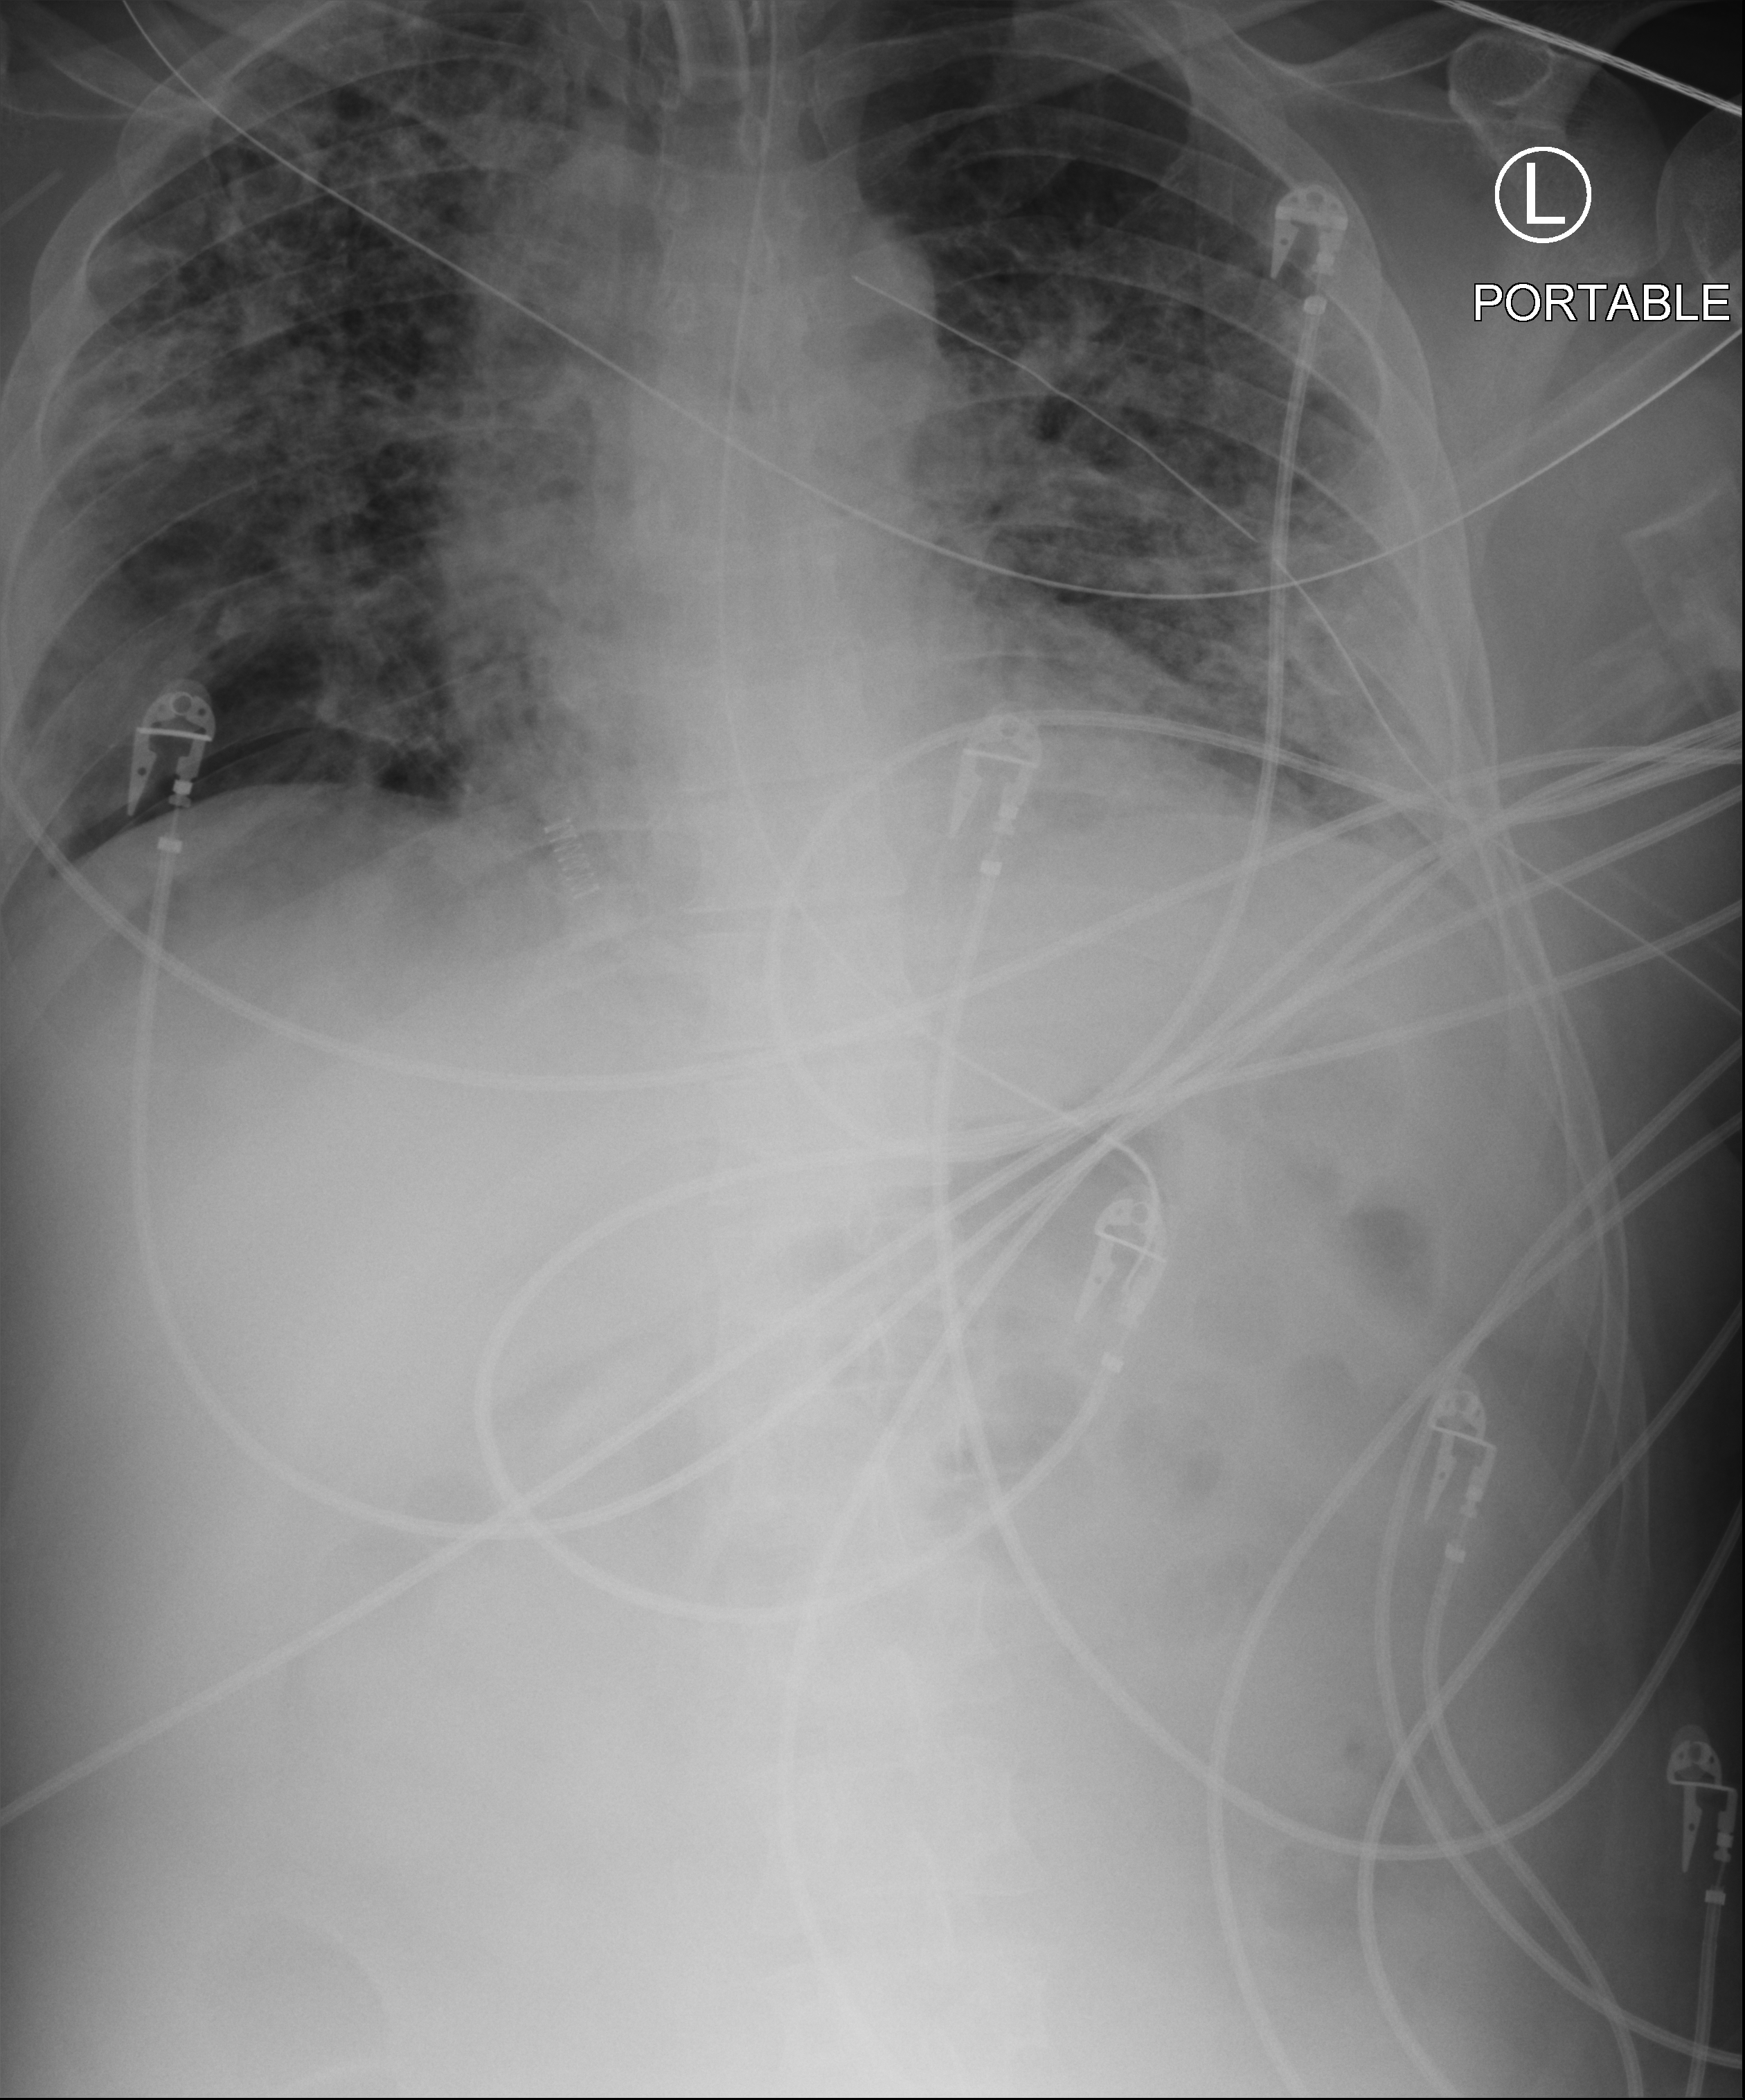
Bedside chest radiograph (computed radiography), anteroposterior (AP) projection. Patient hospitalised with COVID-19; male, aged 18–59 years.
Admission-level facts for this patient (not findings on this image; timing relative to this image not recorded): mechanically ventilated during this hospital stay: yes; admitted to intensive care during this hospital stay: yes; chronic kidney disease (admission record): no.